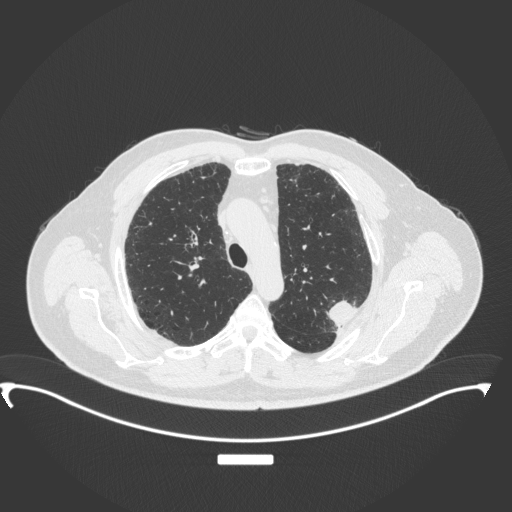
Chest CT, one axial slice. Reconstruction kernel B31f. 120 kVp. Lung window (W 1500 / L -600 HU). 1 mm slice thickness. 512 × 512 image matrix, field of view 459 × 459 mm. Male patient, age 64 years. From the clinical record (not read from this slice): clinical TNM (as recorded): T1c N1 M1.
Structures marked on this image (rectangle marked by the reading radiologist):
- lung tumour (recorded histology: adenocarcinoma): box from (x=317, y=294) to (x=361, y=333) px